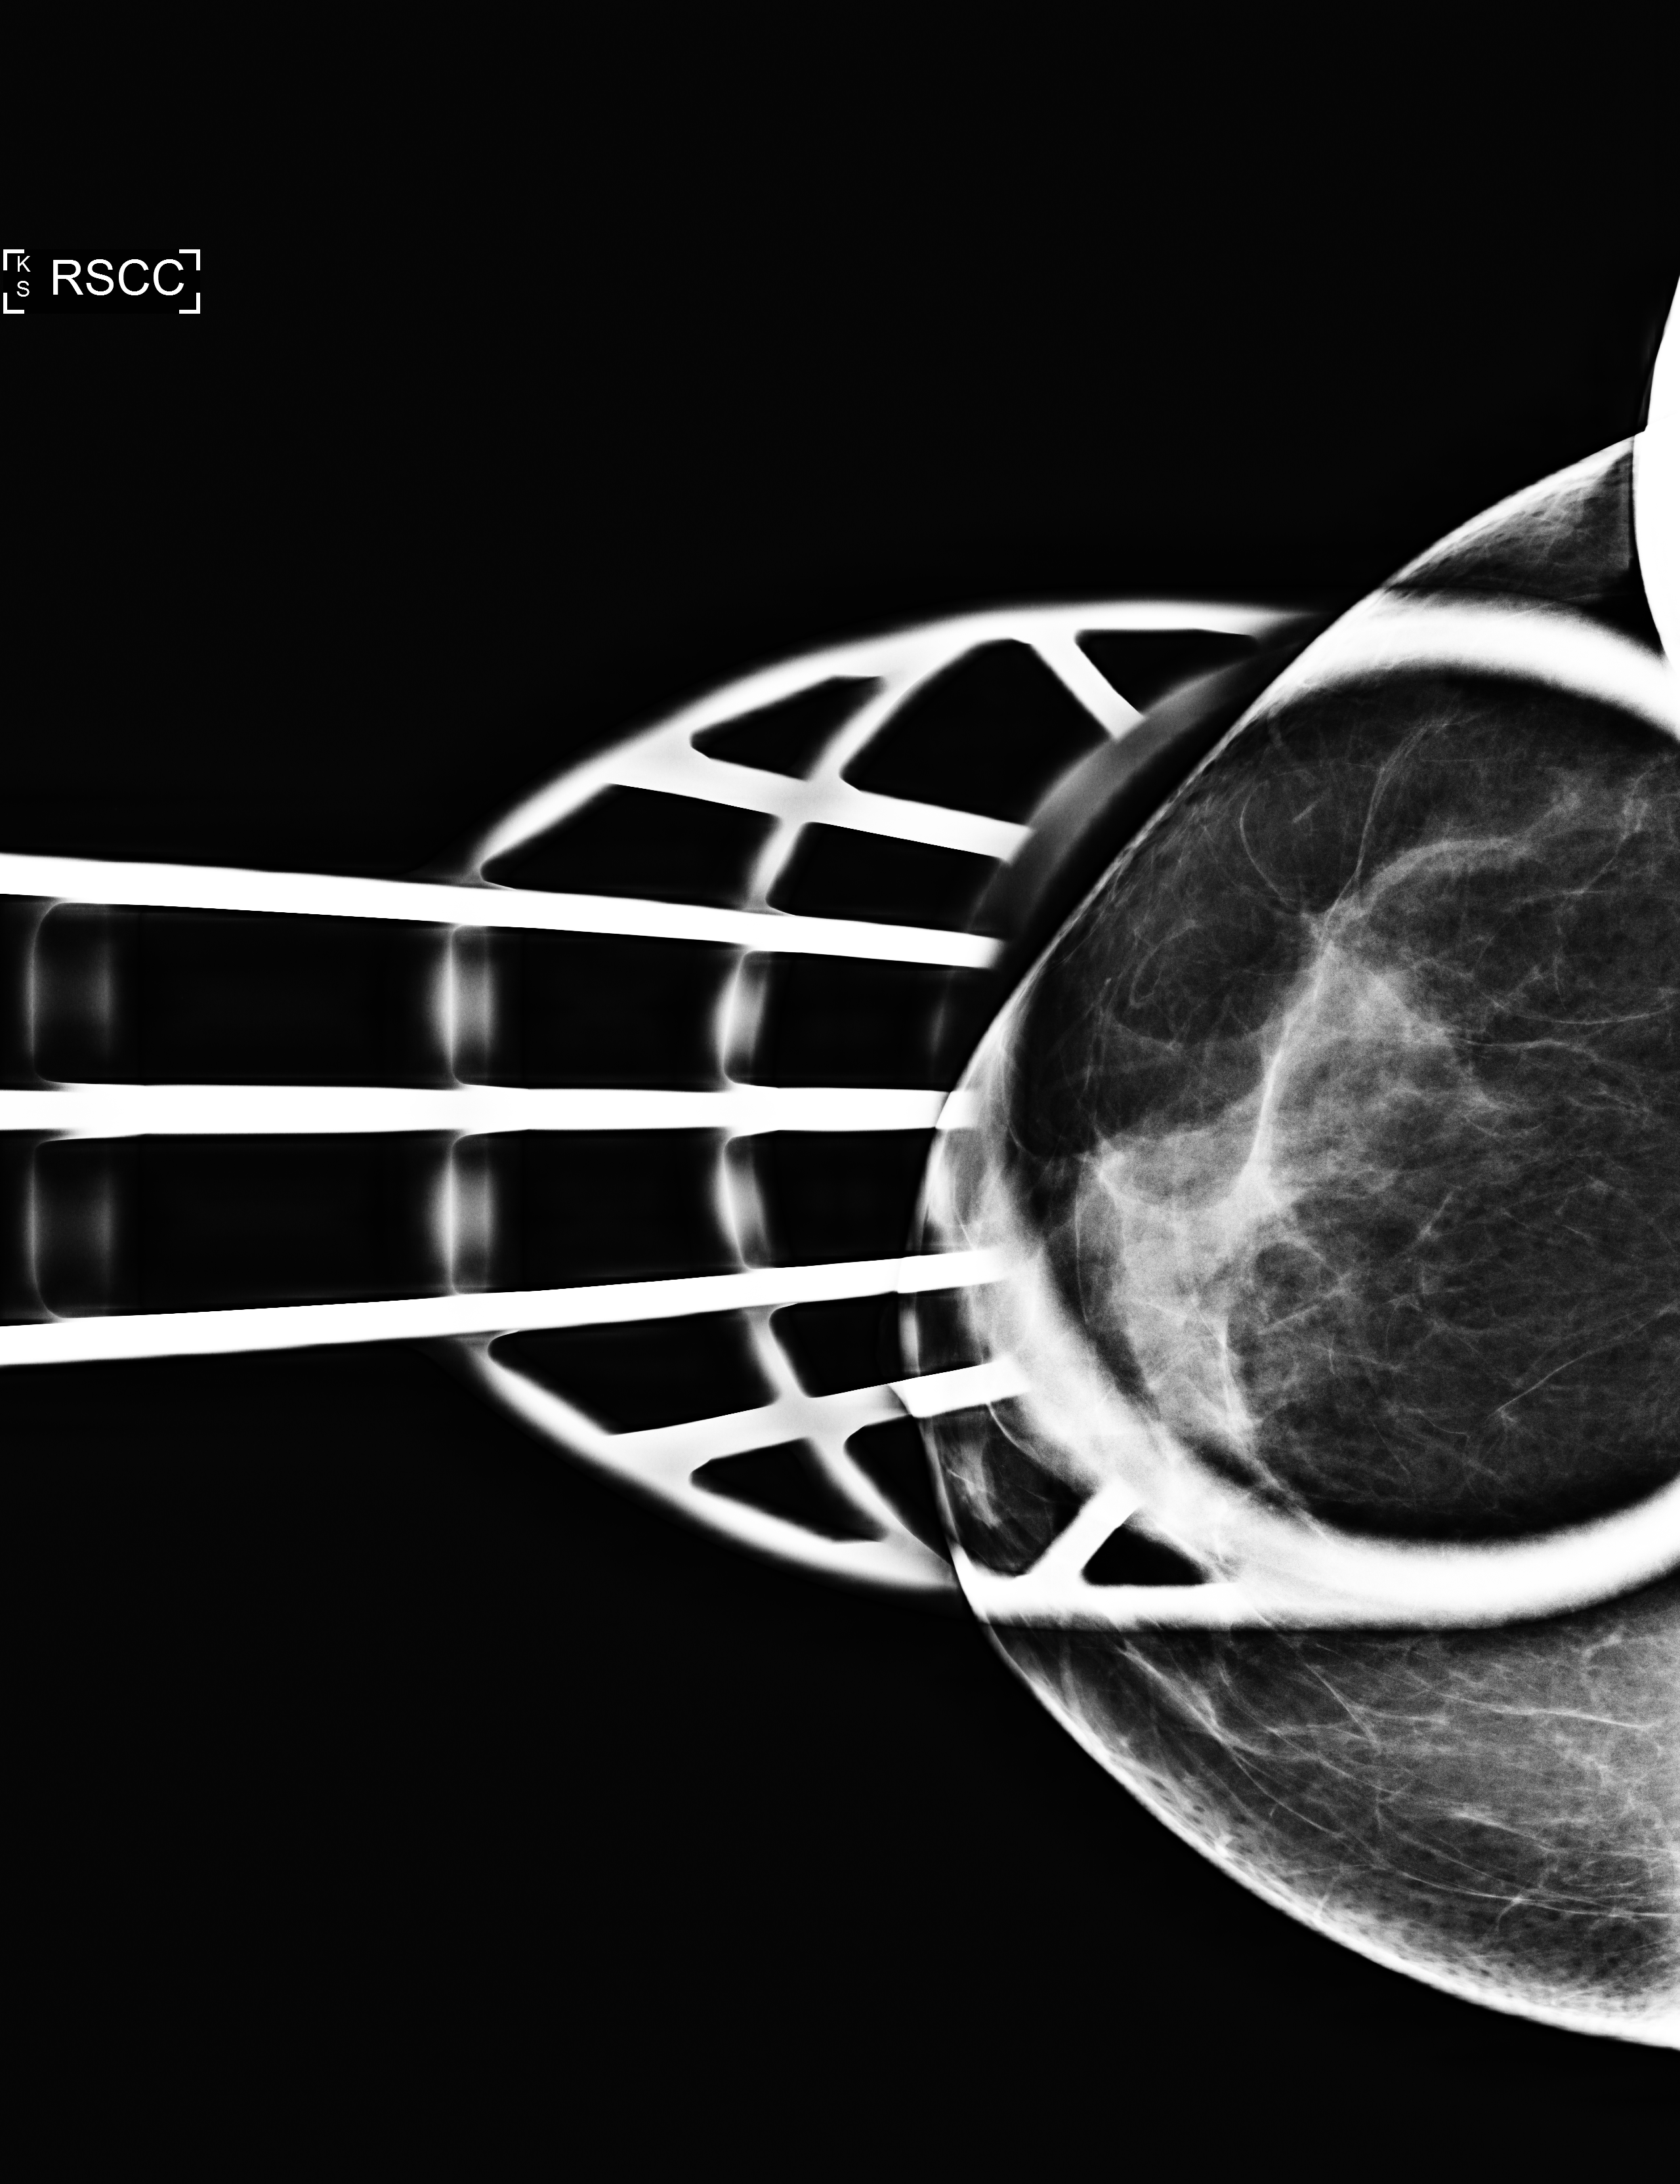
Full-field digital mammogram (FFDM), right breast, craniocaudal (CC) view (spot compression), additional work-up view, compressed breast thickness 55 mm. Patient aged 49 years (female).
- breast density at the screening exam (both breasts): heterogeneously dense (BI-RADS density category c)
- final BI-RADS assessment for this screening round (tomosynthesis exam, both breasts): category 2
- recall: recalled for additional imaging after this screen